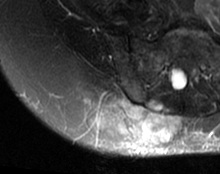
MRI of an extremity soft-tissue mass, one axial slice; slice 44 of 63 in the series (ordered by position); T2-weighted fat-saturated; MR volume resampled by the dataset authors to the PET/CT grid (not the native acquisition matrix); 3.27 mm slice thickness; 220 × 174 image matrix, field of view 215 × 170 mm. Female patient. From the clinical record (not read from this slice): histological type: spindle cell suggestive of myxofibrosarcoma; grade: intermediate; site of the primary tumour: right buttock.
Outlined on this slice (expert contour drawn on MRI and transferred to this co-registered scan by the dataset authors):
- gross tumour volume (mass): bounding box [x1, y1, x2, y2] px = [109, 98, 180, 142]